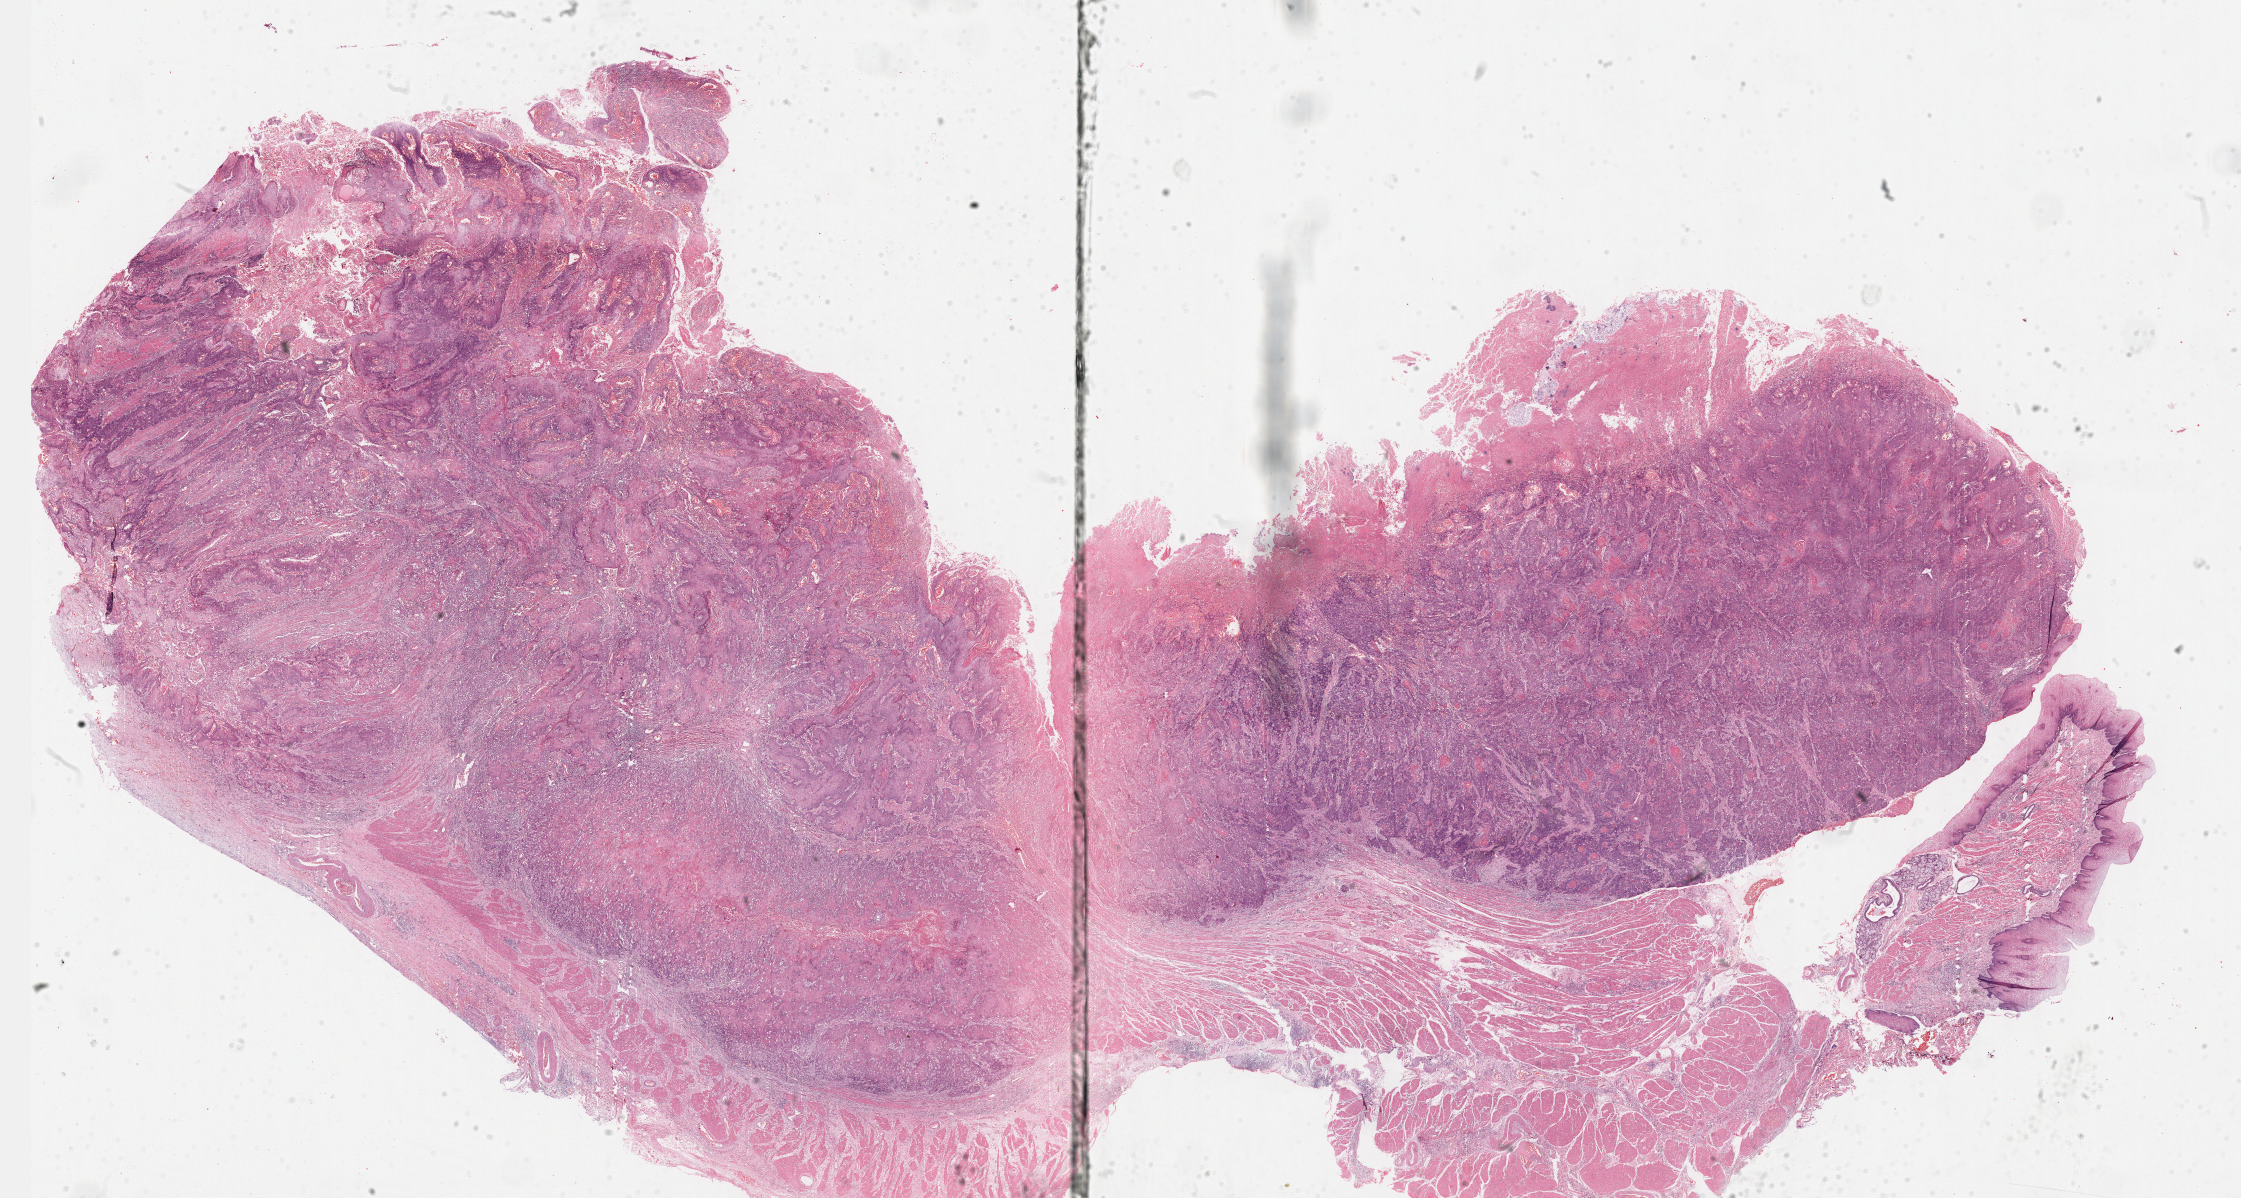
Digitized H&E tissue section (whole slide), a low-resolution overview of the entire scanned area, about 36.2 x 19.4 mm (from a 40x scan); formalin-fixed paraffin-embedded (FFPE) diagnostic section; primary tumour sample from the esophagus. Male patient; age at initial diagnosis 42 years.
Histologic diagnosis: Squamous cell carcinoma, NOS (lower third of esophagus).